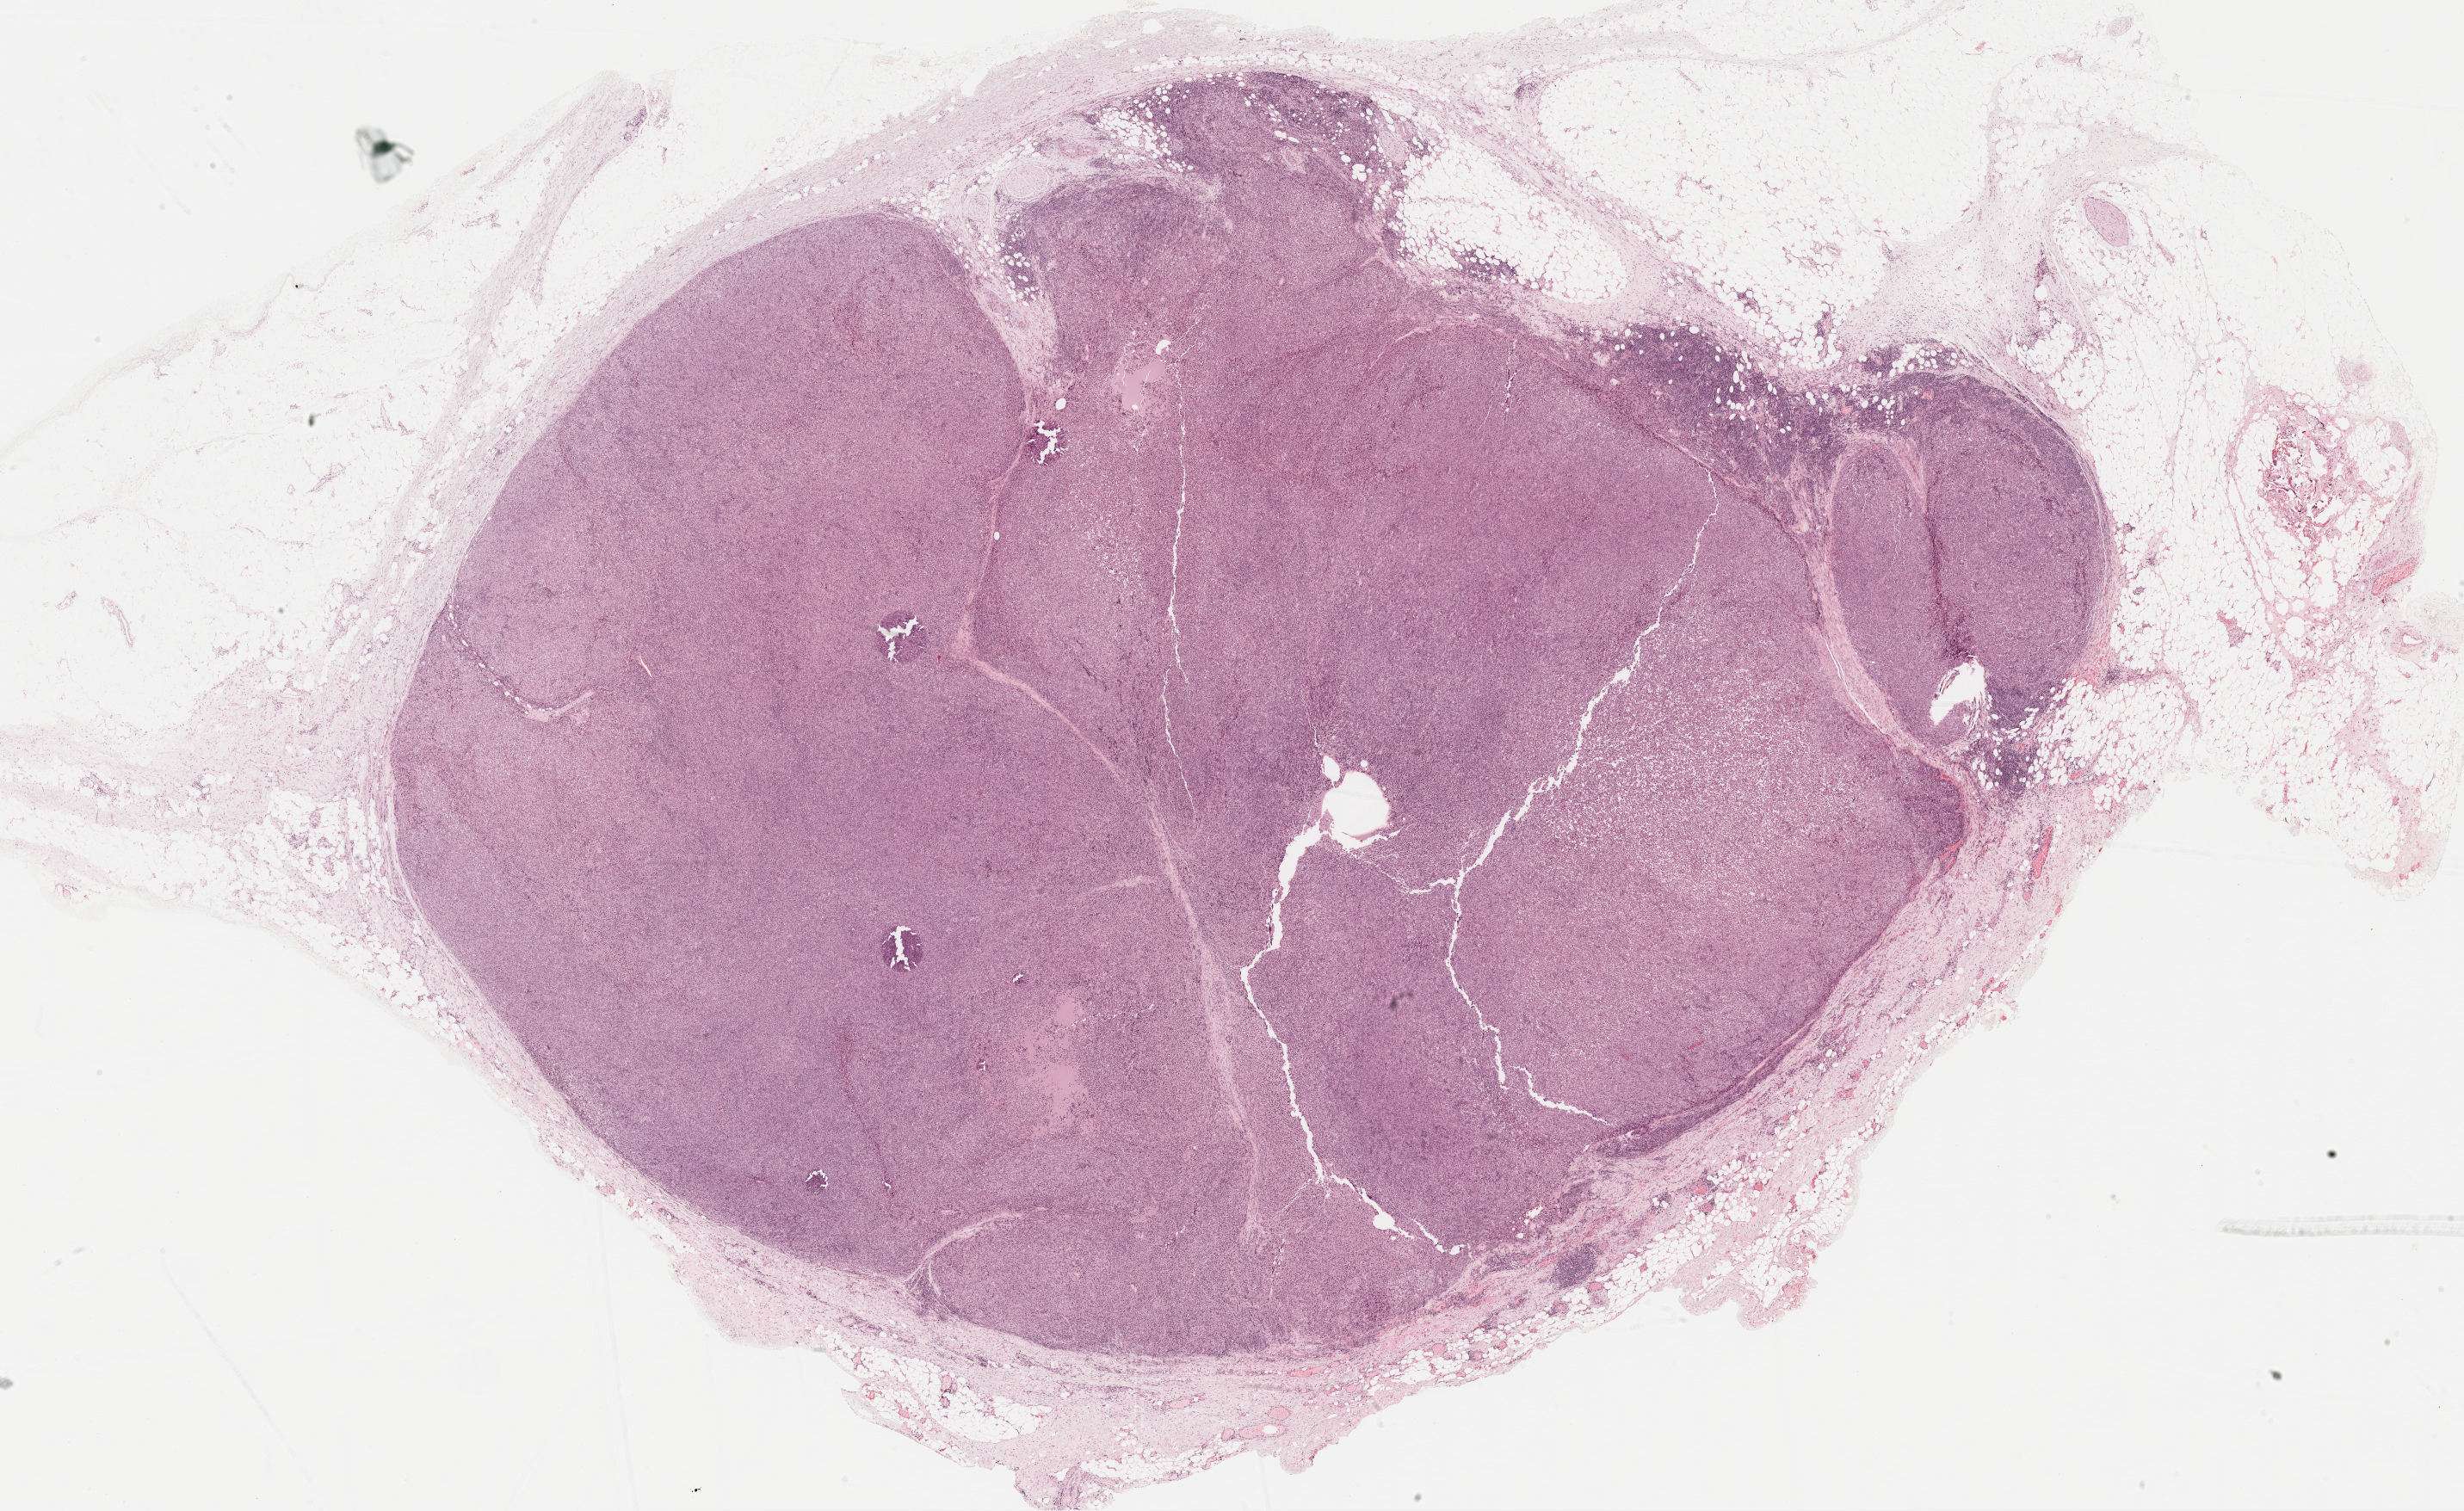
H&E whole-slide image, whole scanned area (about 23.1 x 14.2 mm) shown as a low-resolution overview, formalin-fixed paraffin-embedded (FFPE) diagnostic section, metastatic tumour sample, sampled site not recorded. Patient: female, age at initial diagnosis 43 years.
* this section: metastatic tumour tissue
* patient diagnosis: Malignant melanoma, NOS